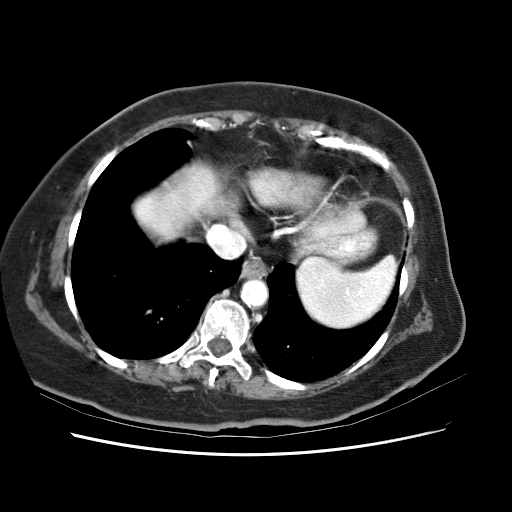
Contrast-enhanced abdominal CT (liver protocol), one axial slice. Slice 57 of 62 in the series (ordered by position). Reconstruction kernel STANDARD. 120 kVp. Soft-tissue window (W 400 / L 40 HU). 2.5 mm slice thickness. 512 × 512 image matrix, field of view 340 × 340 mm. From the clinical record (not read from this slice): diagnosis: hepatocellular carcinoma (patient treated with transarterial chemoembolisation; whether this scan precedes or follows treatment is not stated here); TNM stage (as recorded): Stage-I; Child-Pugh class: B; tumour nodularity: uninodular.
Annotated regions visible in this slice (semi-automatic segmentation, software-assisted and operator-edited):
- liver parenchyma outside the tumour (the mass and vessels are separate outlines, so this box may not span the whole liver): bounding box <182,177,210,210> (left, top, right, bottom; pixels)